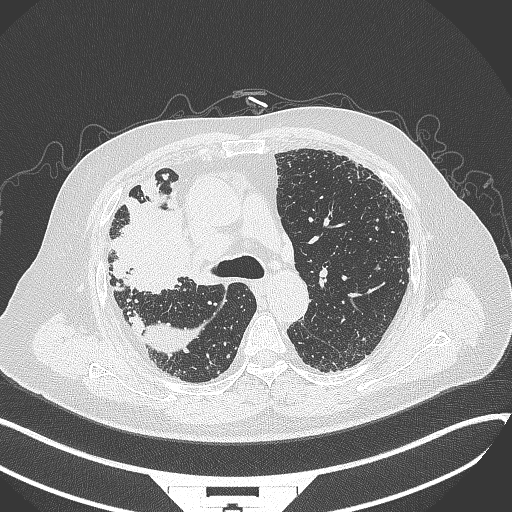
Chest CT, one axial slice; position 233 of 384 along the scan axis; reconstruction kernel B70f; lung window (W 1500 / L -600 HU); 512 × 512 image matrix, field of view 400 × 400 mm. Male patient, age 69 years. From the clinical record (not read from this slice): clinical TNM (as recorded): T4 N3 M1.
Outlined on this slice (bounding box drawn by a radiologist):
- lung tumour (recorded histology: adenocarcinoma): box from (x=112, y=189) to (x=200, y=296) px